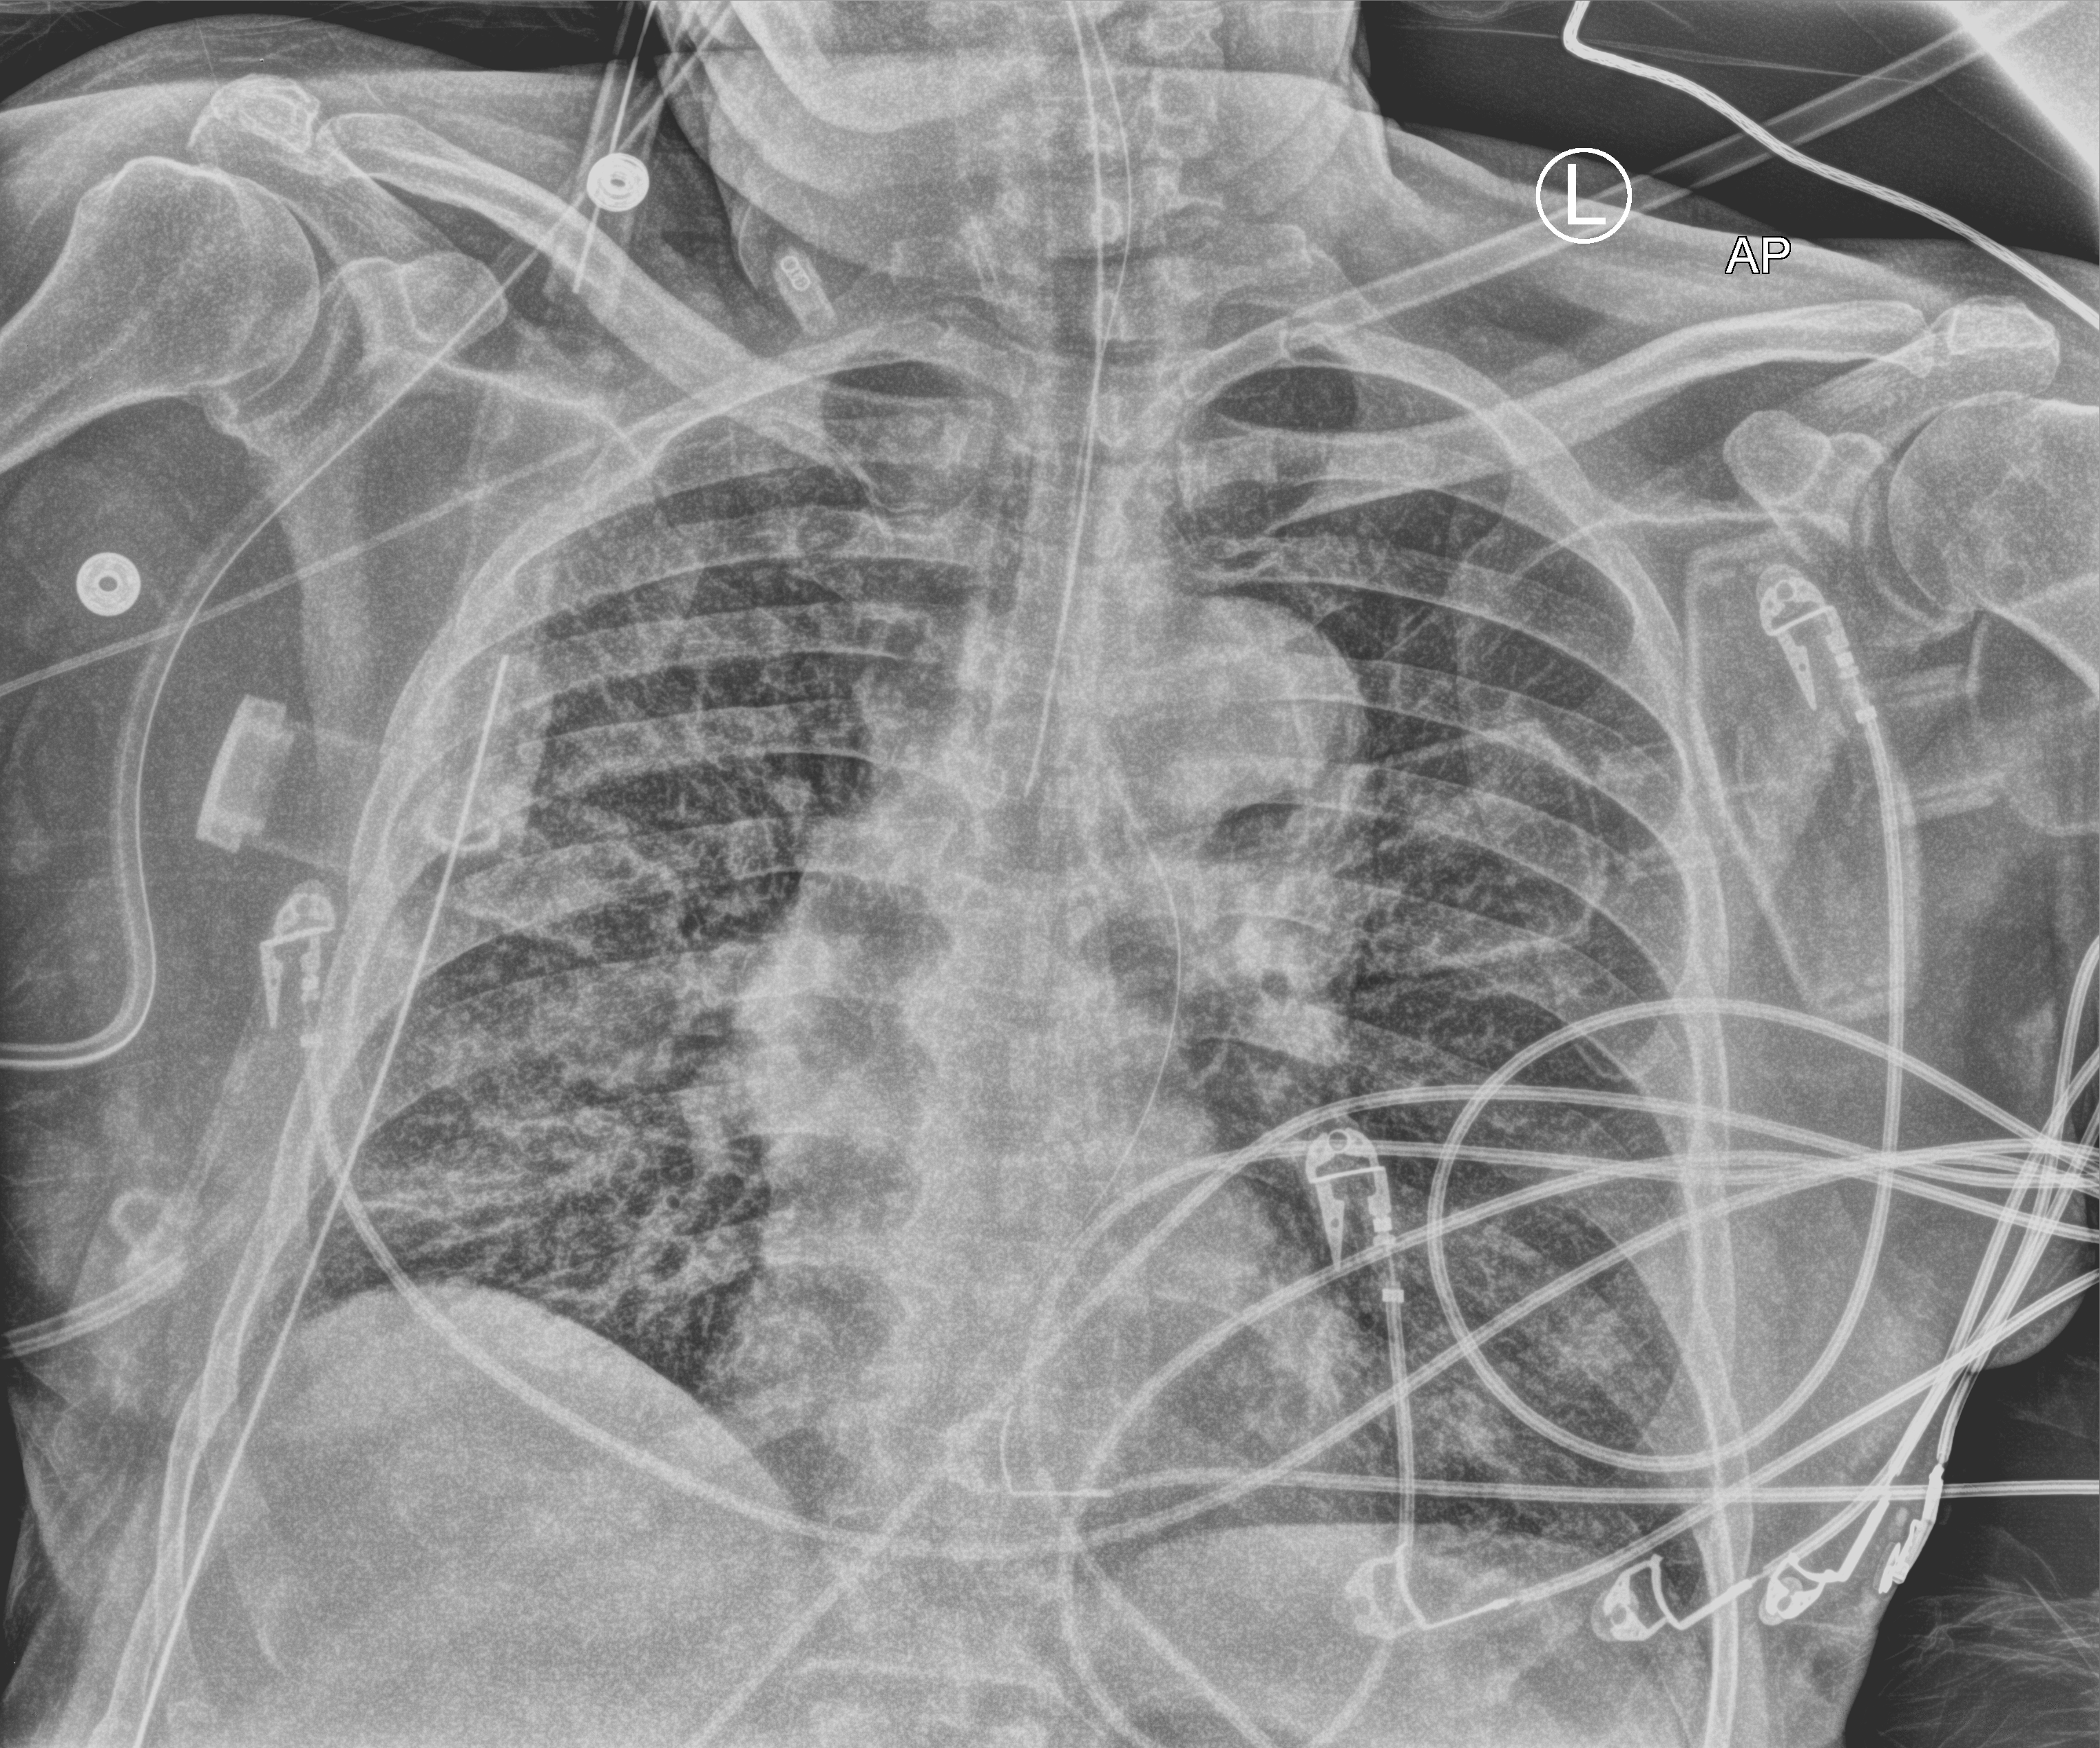
Portable chest radiograph, anteroposterior (AP) projection. Patient hospitalised with COVID-19; male, aged 60–74 years.
Hospital-stay facts (about this admission, not read from this image; timing relative to this image not recorded): mechanically ventilated during this hospital stay: yes.